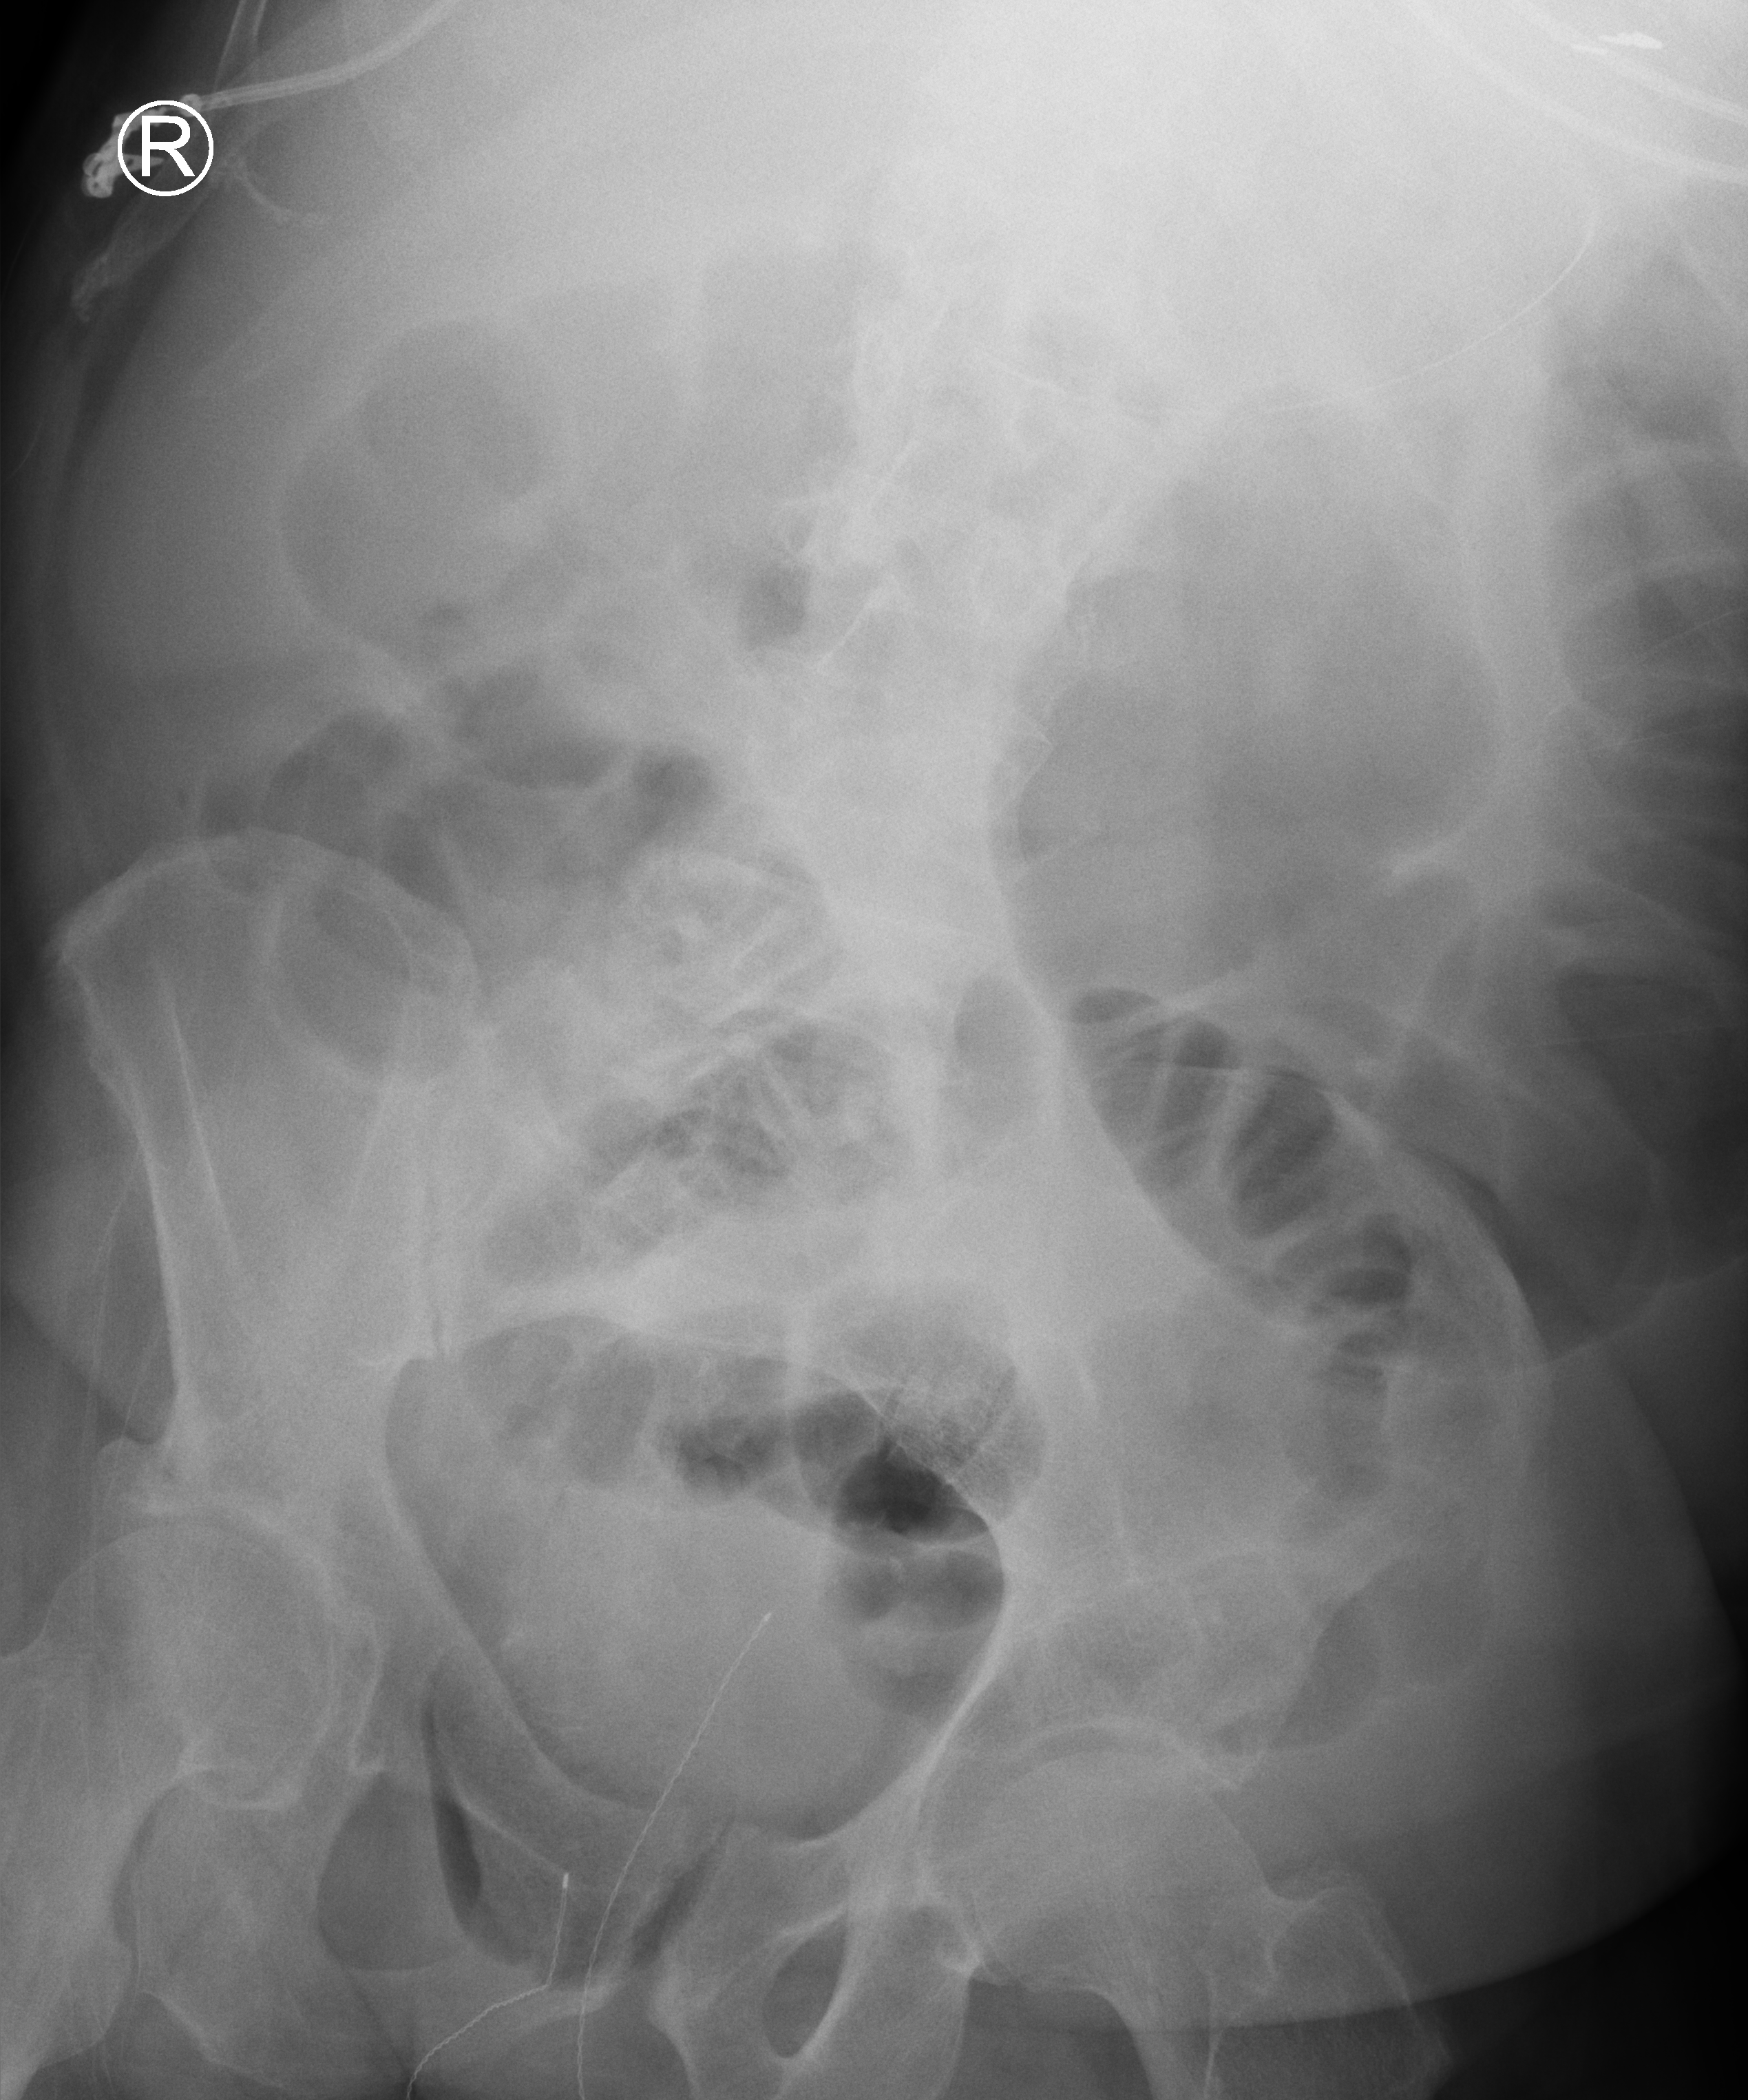
Abdomen X-ray (portable); anteroposterior (AP) projection. Patient hospitalised with COVID-19; male, aged 60–74 years.
Hospital-stay facts (about this admission, not read from this image; timing relative to this image not recorded): diabetes (admission record): yes.